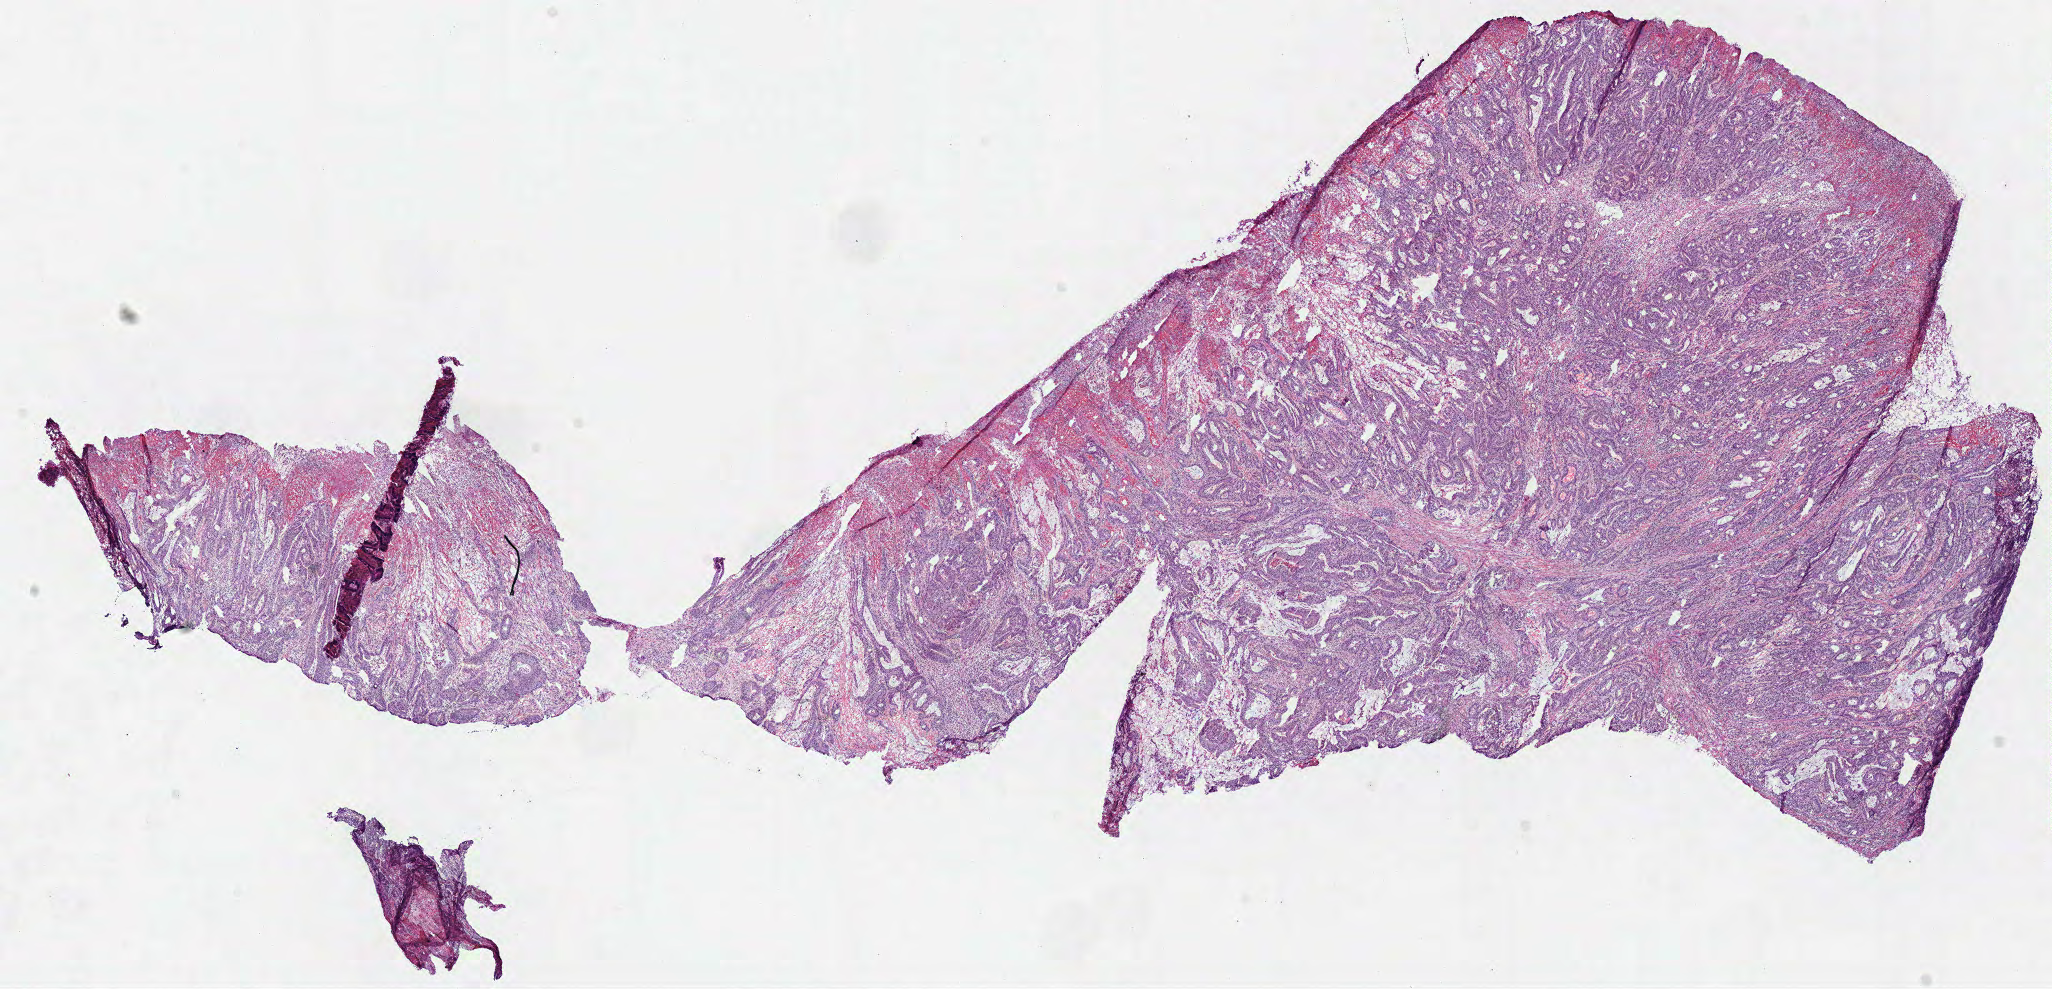
Whole-slide histology image, H&E-stained — low-resolution overview of the scanned area, about 16.2 x 7.8 mm; frozen section; colon, primary tumour sample. Patient: male, age at initial diagnosis 34 years. Pathologist review of this section (percent, as recorded): tumour cells 67%, tumour nuclei 75%, normal cells 0%, stromal cells 21%, necrosis 12%. Infiltration values recorded for this section: lymphocyte infiltration 10%, monocyte infiltration 2%, neutrophil infiltration 3%.
- pathologic diagnosis: Adenocarcinoma, NOS (sigmoid colon)
- TNM: T3 N0 M0
- AJCC pathologic stage: IIA